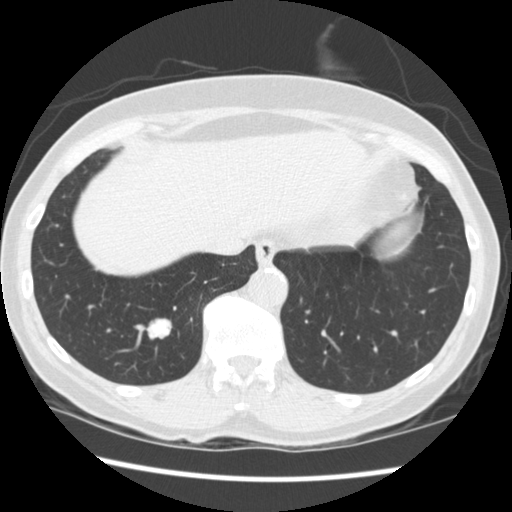
Low-dose screening chest CT, one axial slice; position 62 of 262 along the scan axis; reconstruction kernel STANDARD; lung window (W 1500 / L -600 HU); 2.5 mm slice thickness; 512 × 512 image matrix.
Outlined on this slice (expert manual segmentation):
- lesion 1 (tumor, lower lobe of right lung): box from (x=147, y=319) to (x=172, y=339) px